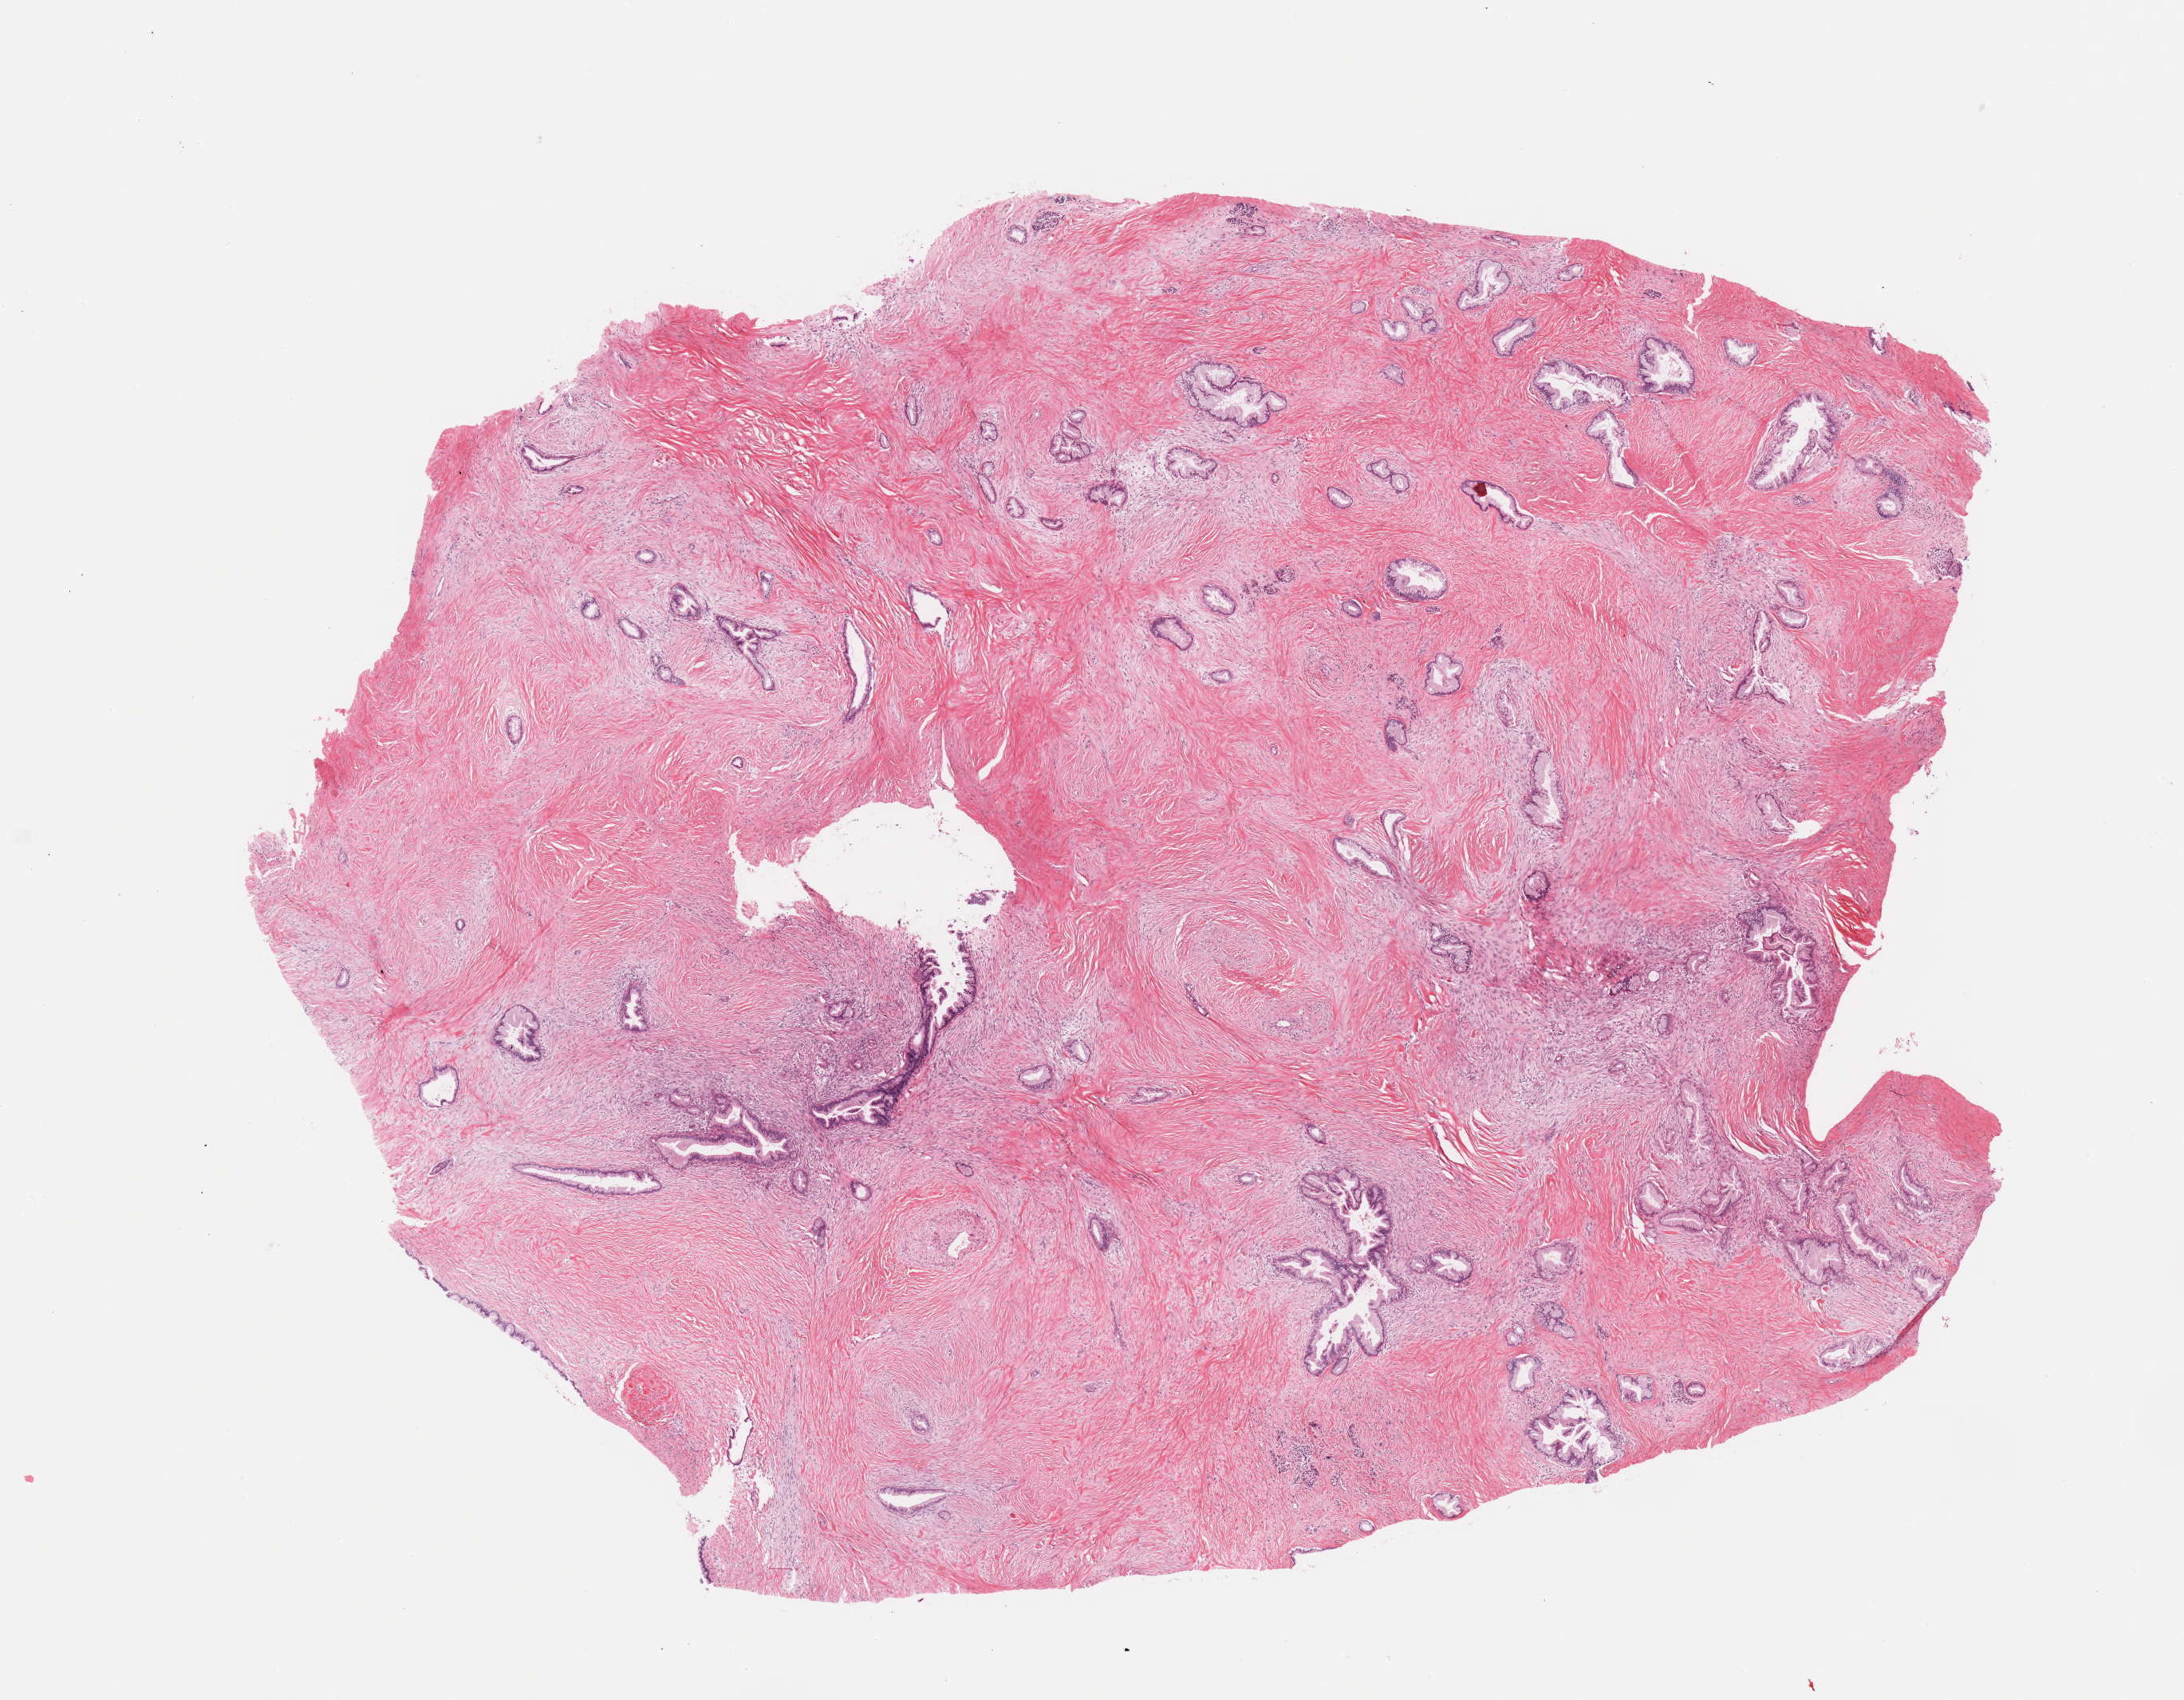
Digitized H&E-stained tissue section (whole slide), whole scanned area (about 10.8 x 8.4 mm, acquisition: 20x scan) shown as a low-resolution overview, tumour tissue sample, sampled site: pancreas. Male, 69 y/o. Histologic grade: G2 (moderately differentiated). Composition of this section per pathologist review: tumour nuclei 30%, necrosis 0%.
- diagnosis: Infiltrating duct carcinoma, NOS
- AJCC pathologic stage: IIB
- primary tumour site (as recorded): body